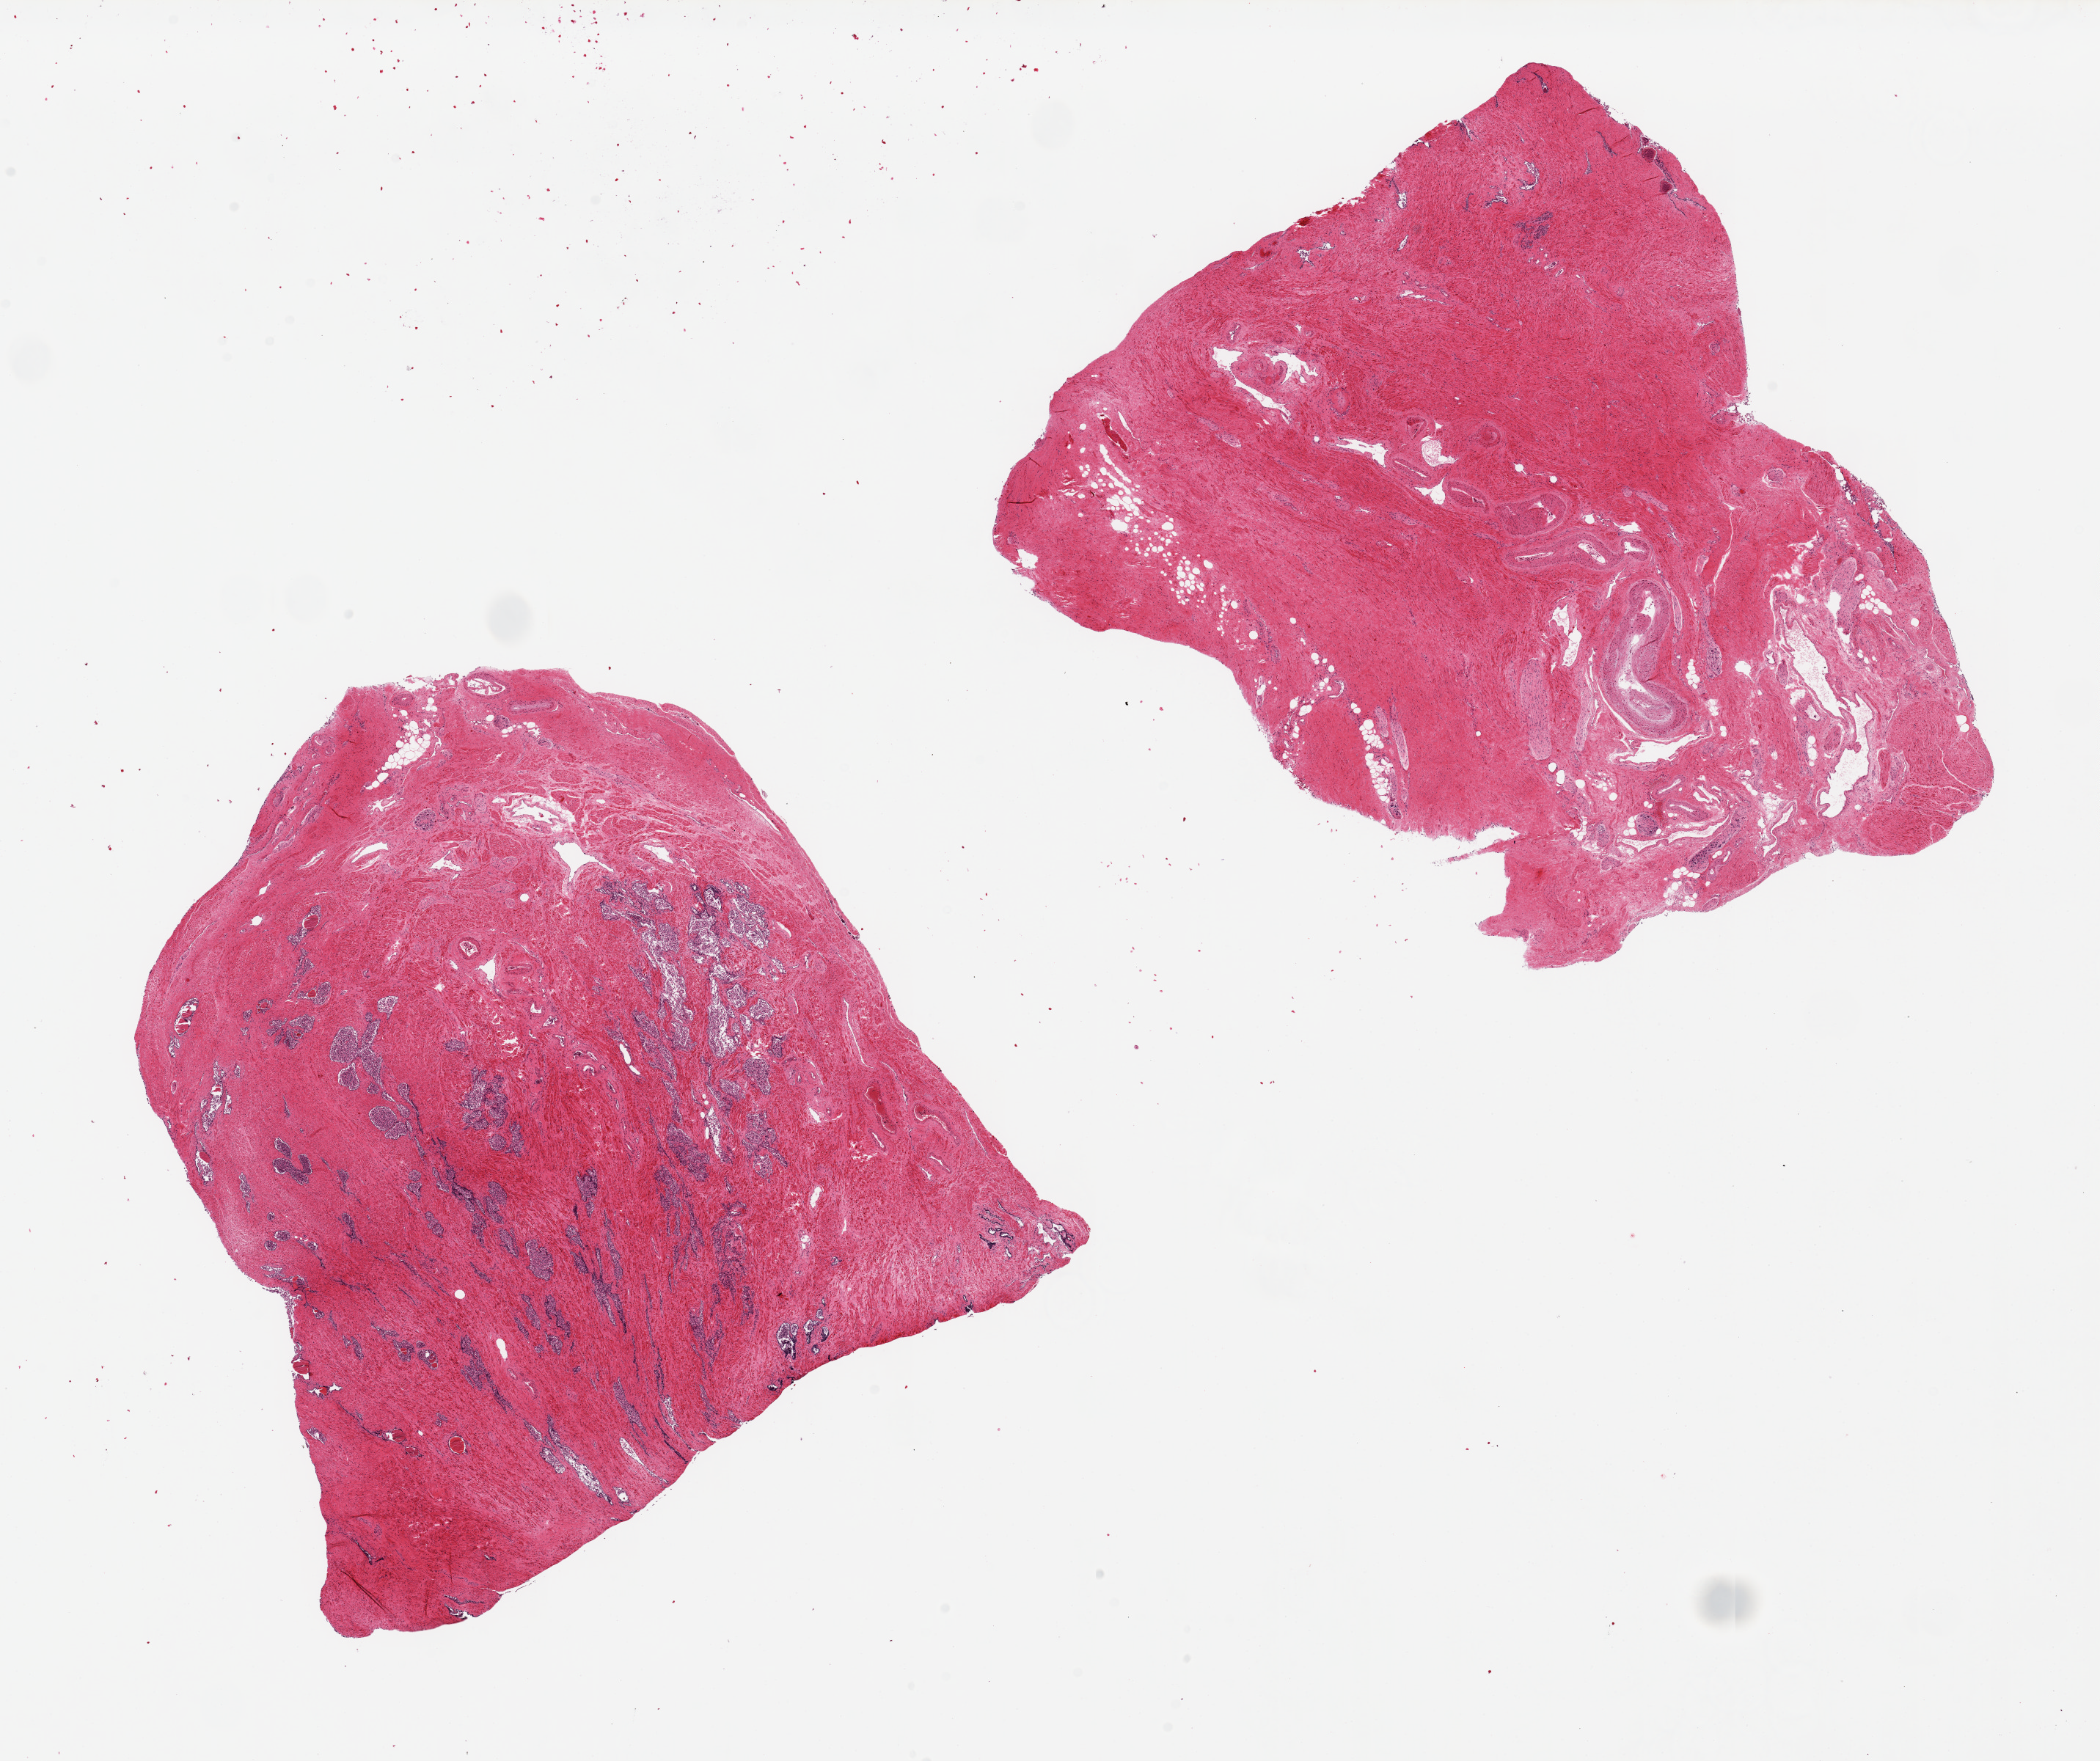
Whole-slide image, hematoxylin and eosin (H&E) stain — whole scanned area (about 22.6 x 19.0 mm) shown as a low-resolution overview; PAXgene-fixed paraffin-embedded (PFPE) section; section of prostate (target tissue); tissue donor sample. Donor: male.
- reviewer comment on this tissue sample: 2 pieces, up to 9x9mm; one with badly autolyzed glands, the other is all stroma